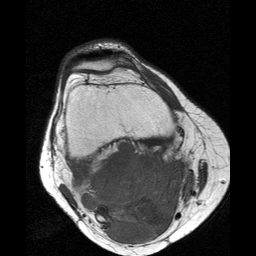
MRI of an extremity soft-tissue mass, one axial slice. Position 13 of 25 along the scan axis. 256 × 256 image matrix. Female patient. Case-level facts recorded for this patient, not image findings: histological type: liposarcoma; site of the primary tumour: right thigh.
Structures marked on this image (expert manual segmentation):
- gross tumour volume (mass): bounding box [x1, y1, x2, y2] px = [81, 142, 191, 243]